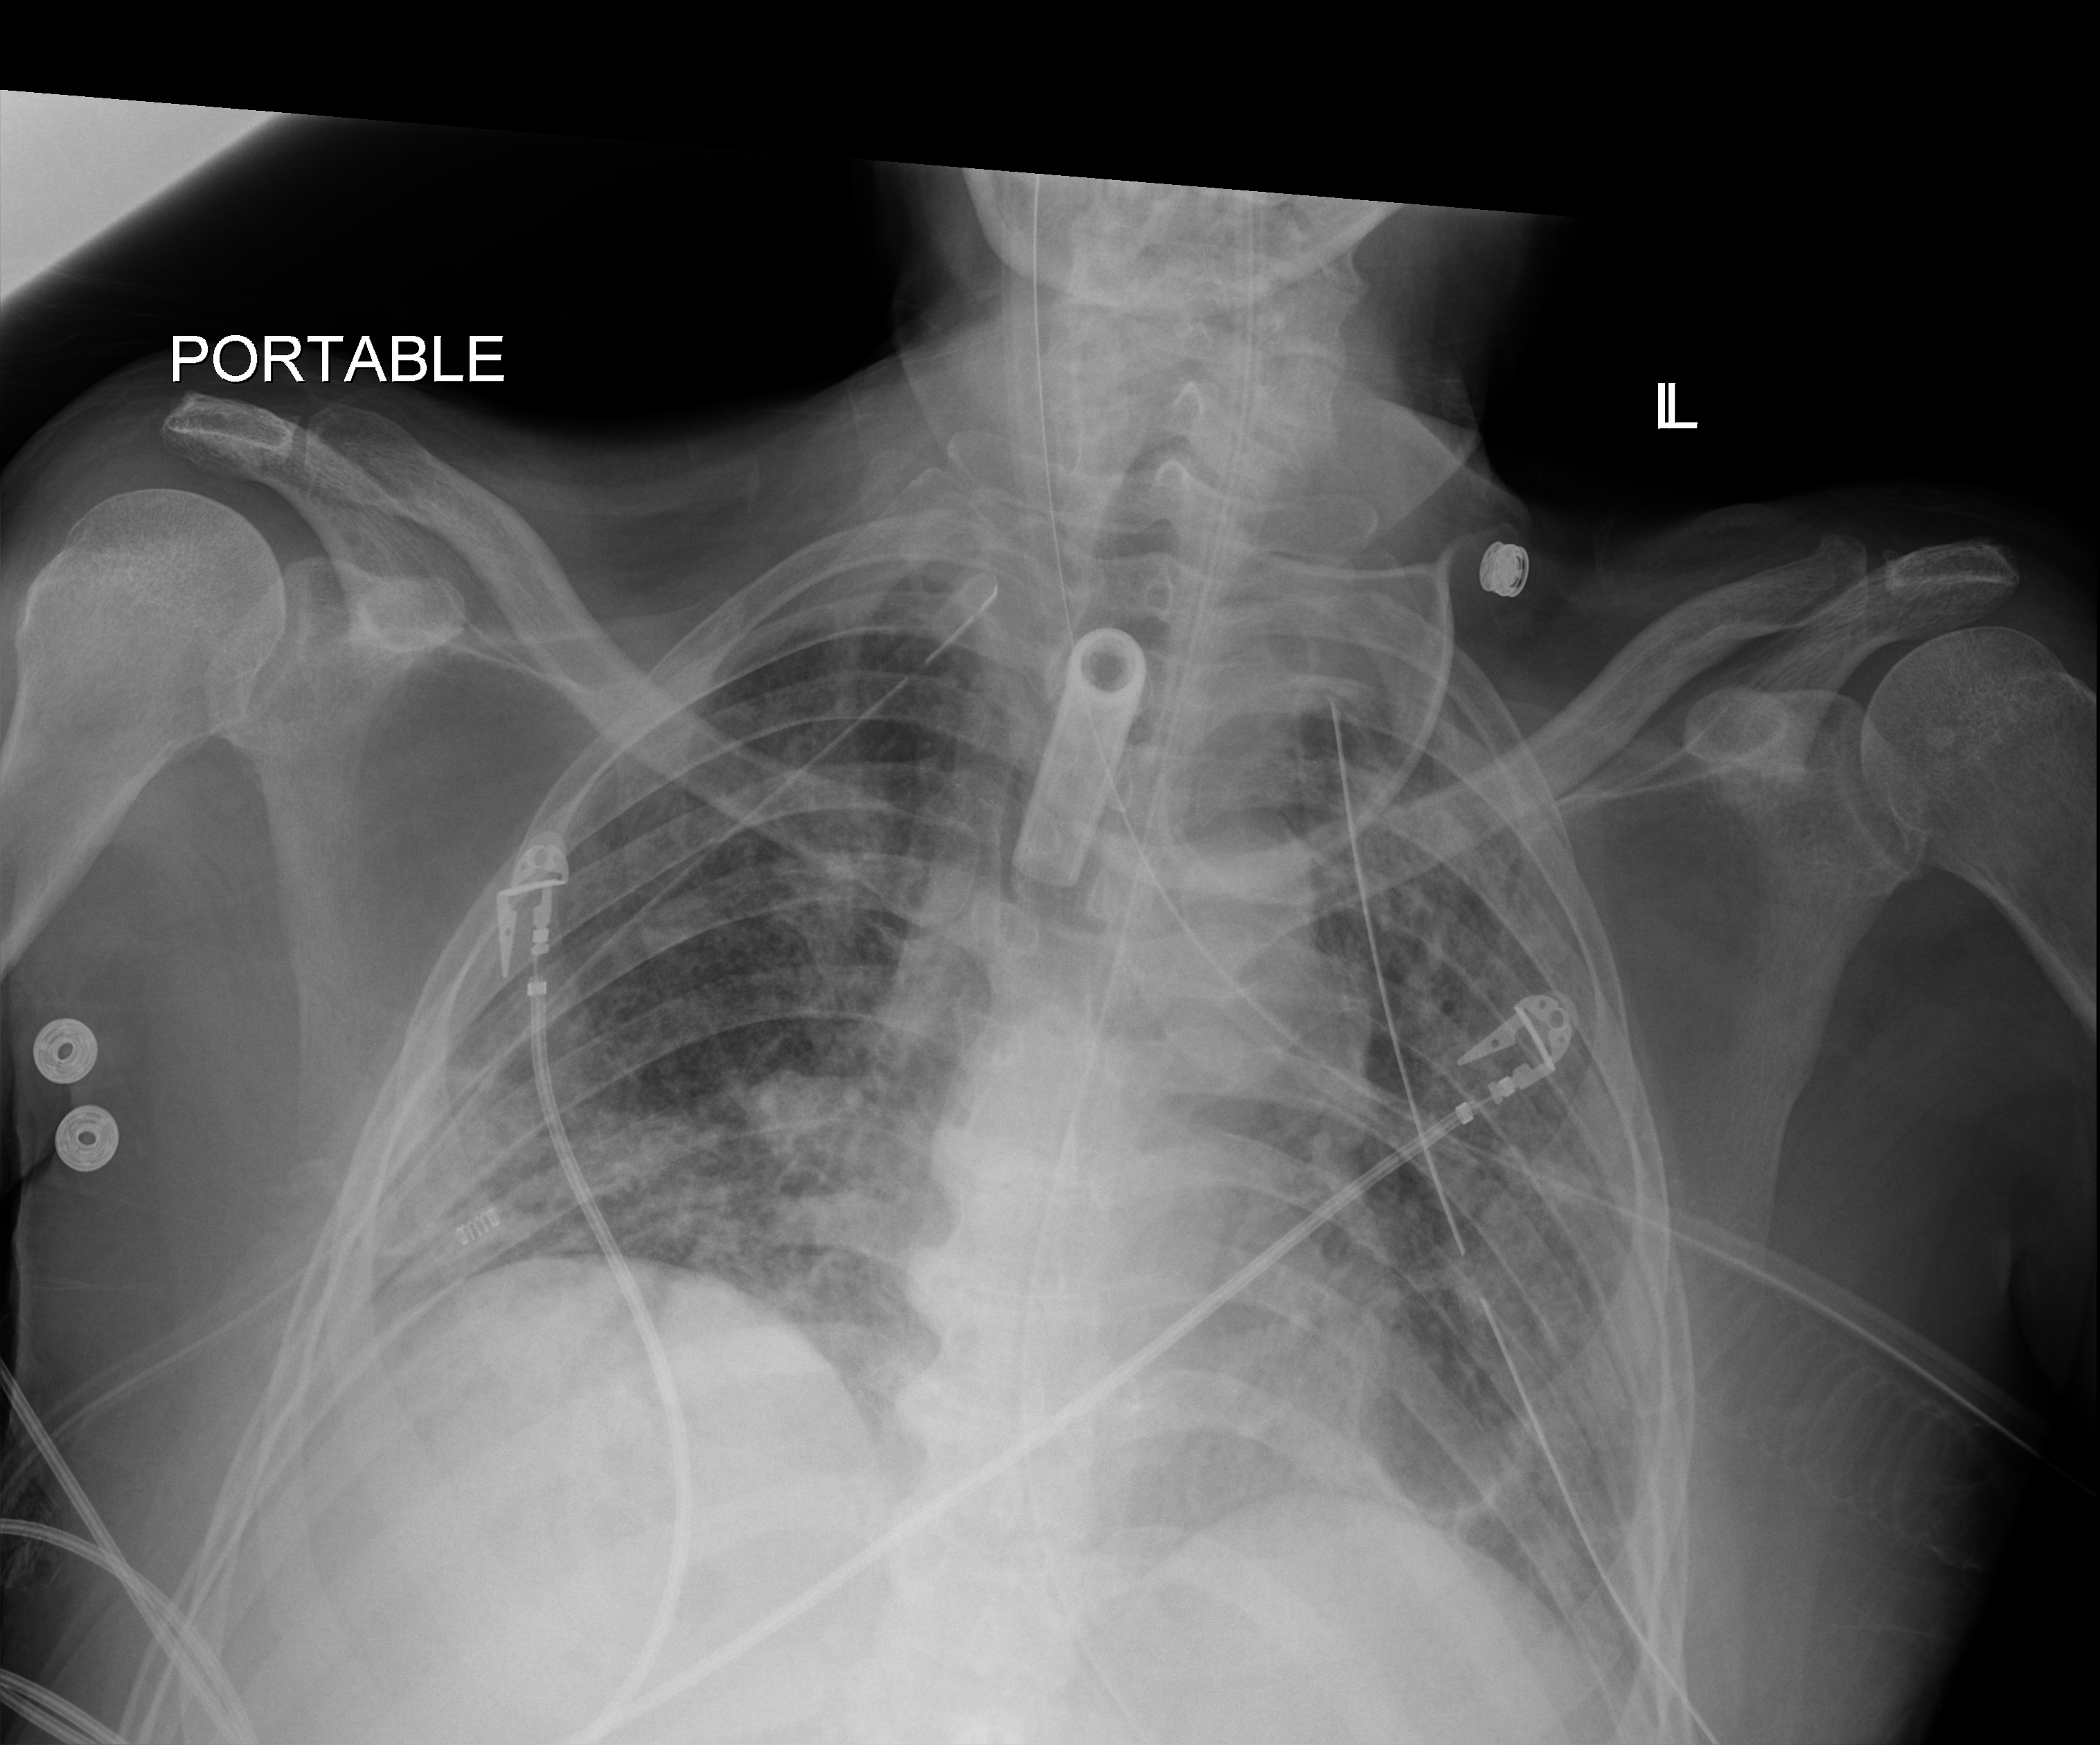
Chest X-ray (portable); anteroposterior (AP) projection. Patient hospitalised with COVID-19; male, aged 18–59 years.
From the hospital-stay record, not from the radiograph (when in the stay this image was taken is not recorded): mechanically ventilated during this hospital stay: yes; length of hospital stay: 83 days.